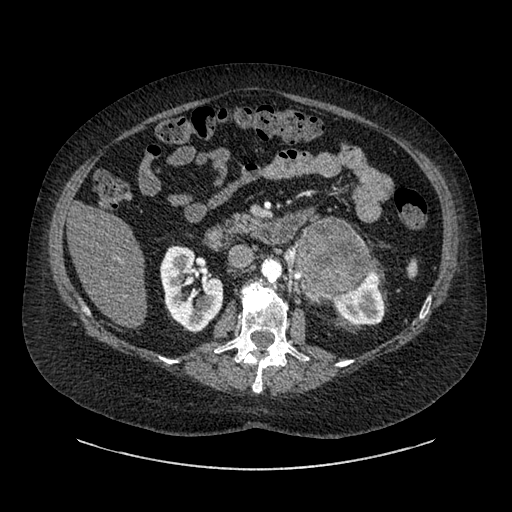
Contrast-enhanced abdominal CT, one axial slice. Intravenous contrast given. Soft-tissue window (W 400 / L 40 HU). 512 × 512 image matrix. Patient: female, 61 years. From the clinical record (not read from this slice): diagnosis: adrenocortical carcinoma; tumour side: left adrenal; tumour size at pathology: 13 cm; Ki-67 index: 79 %.
Annotated regions visible in this slice (semi-automatically segmented with operator editing):
- mass: box from (x=297, y=223) to (x=369, y=296) px